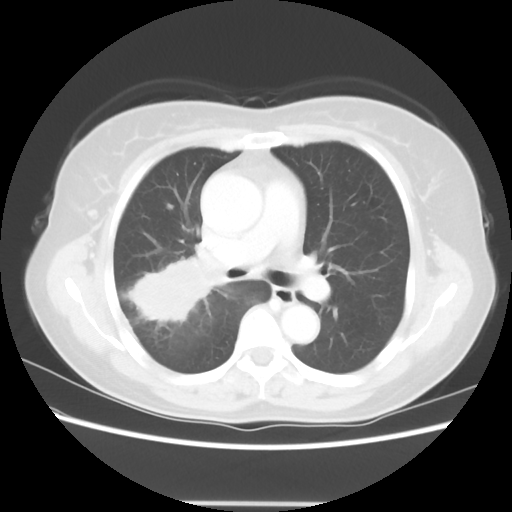
Chest CT, one axial slice; position 36 of 56 along the scan axis; reconstruction kernel STANDARD; lung window (W 1500 / L -600 HU); 5 mm slice thickness; 512 × 512 image matrix. Patient: female, 55 years. From the clinical record (not read from this slice): clinical TNM (as recorded): T2 N1 M0.
Annotated regions visible in this slice (rectangle marked by the reading radiologist):
- lung tumour (recorded histology: adenocarcinoma): bounding box <109,242,228,333> (left, top, right, bottom; pixels)